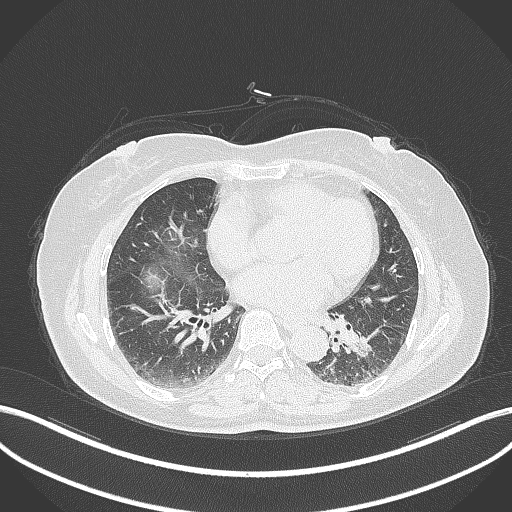
Chest CT, one axial slice. Reconstruction kernel B70f. 120 kVp. Lung window (W 1500 / L -600 HU). 512 × 512 image matrix, field of view 400 × 400 mm. Patient: female, 59 years. Case-level facts recorded for this patient, not image findings: clinical TNM (as recorded): T2a N0 M0; histopathological grade: G2-3.
Outlined on this slice (bounding box drawn by a radiologist):
- lung tumour (recorded histology: adenocarcinoma): box from (x=337, y=315) to (x=386, y=360) px